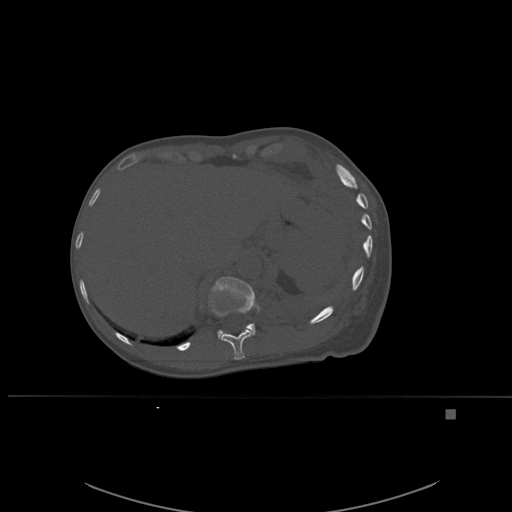
CT including the spine, one axial slice; position 292 of 537 along the scan axis; bone window (W 1800 / L 400 HU); 1.5 mm slice thickness; 512 × 512 image matrix, field of view 440 × 440 mm. Female patient, age 45 years. From the clinical record (not read from this slice): primary cancer: lung.
Annotated regions visible in this slice (semi-automatic segmentation, software-assisted and operator-edited):
- T11 vertebra: bounding box <209,292,253,360> (left, top, right, bottom; pixels)
- T12 vertebra: <211,277,260,339>